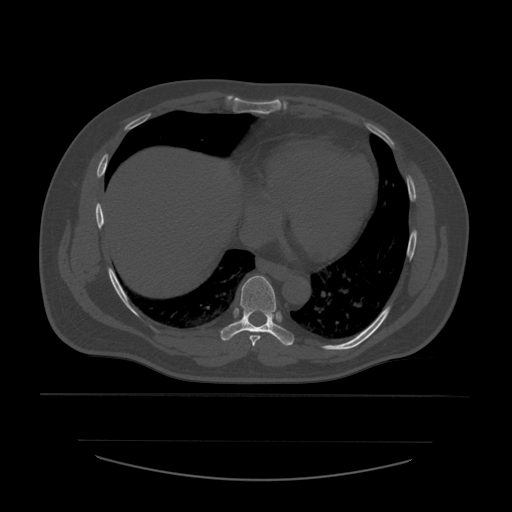
CT including the spine, one axial slice. Position 341 of 532 along the scan axis. Reconstruction kernel STANDARD. Bone window (W 1800 / L 400 HU). 1.25 mm slice thickness. 512 × 512 image matrix, field of view 441 × 441 mm. Patient age 44 years. Case-level facts recorded for this patient, not image findings: primary cancer: soft tissue sarcoma.
Annotated regions visible in this slice (semi-automatically segmented with operator editing):
- T7 vertebra: box from (x=250, y=335) to (x=261, y=347) px
- T8 vertebra: (x=221, y=276)–(x=294, y=346)